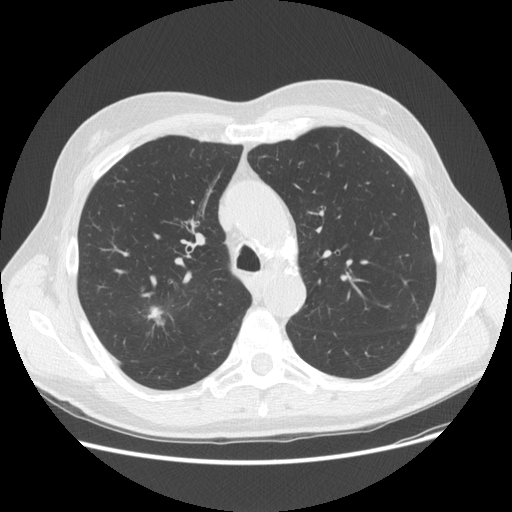
Low-dose screening chest CT, one axial slice; slice 109 of 156 in the series (ordered by position); lung window (W 1500 / L -600 HU); 2.5 mm slice thickness; 512 × 512 image matrix, field of view 380 × 380 mm.
Outlined on this slice (manually delineated by an expert):
- lesion 1 (tumor, upper lobe of right lung): box from (x=147, y=306) to (x=164, y=328) px